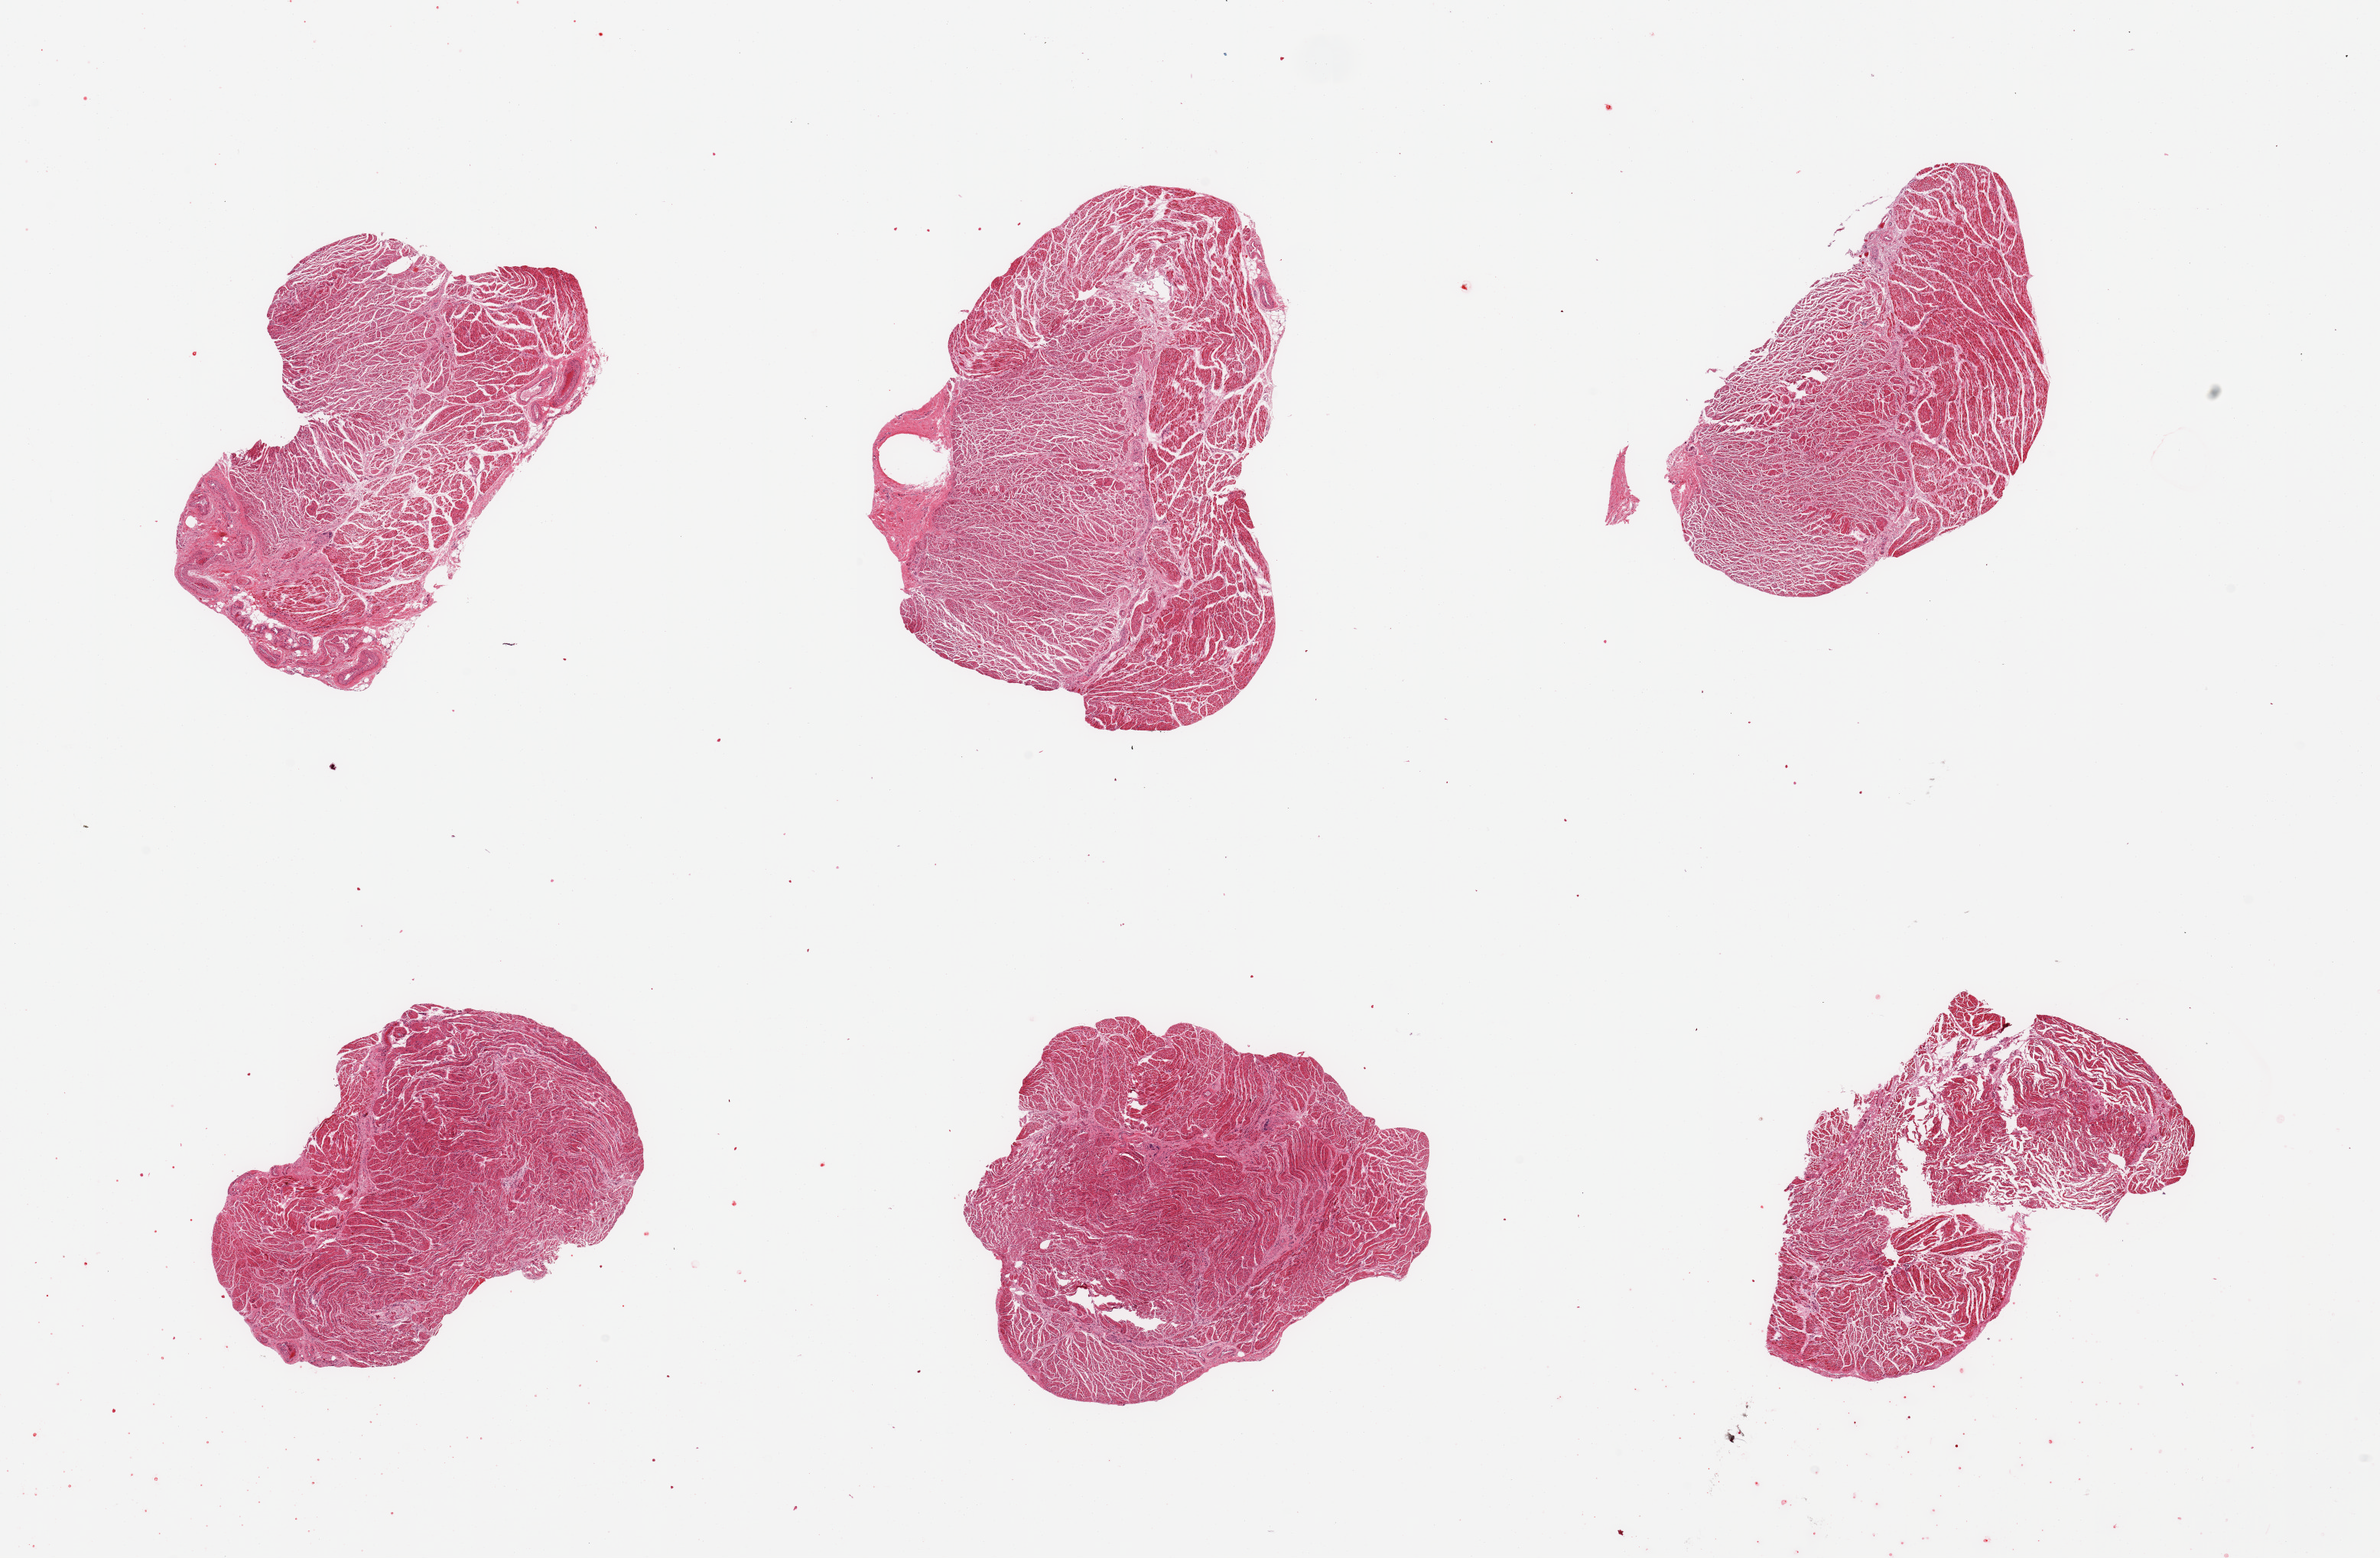
H&E whole-slide image, shown as a low-resolution overview of the whole scanned area (about 24.6 x 16.1 mm); PAXgene-fixed, paraffin-embedded tissue; sampled site (target tissue): gastroesophageal junction; tissue donor sample.
• review note (as recorded): 6 pieces; well dissected muscle